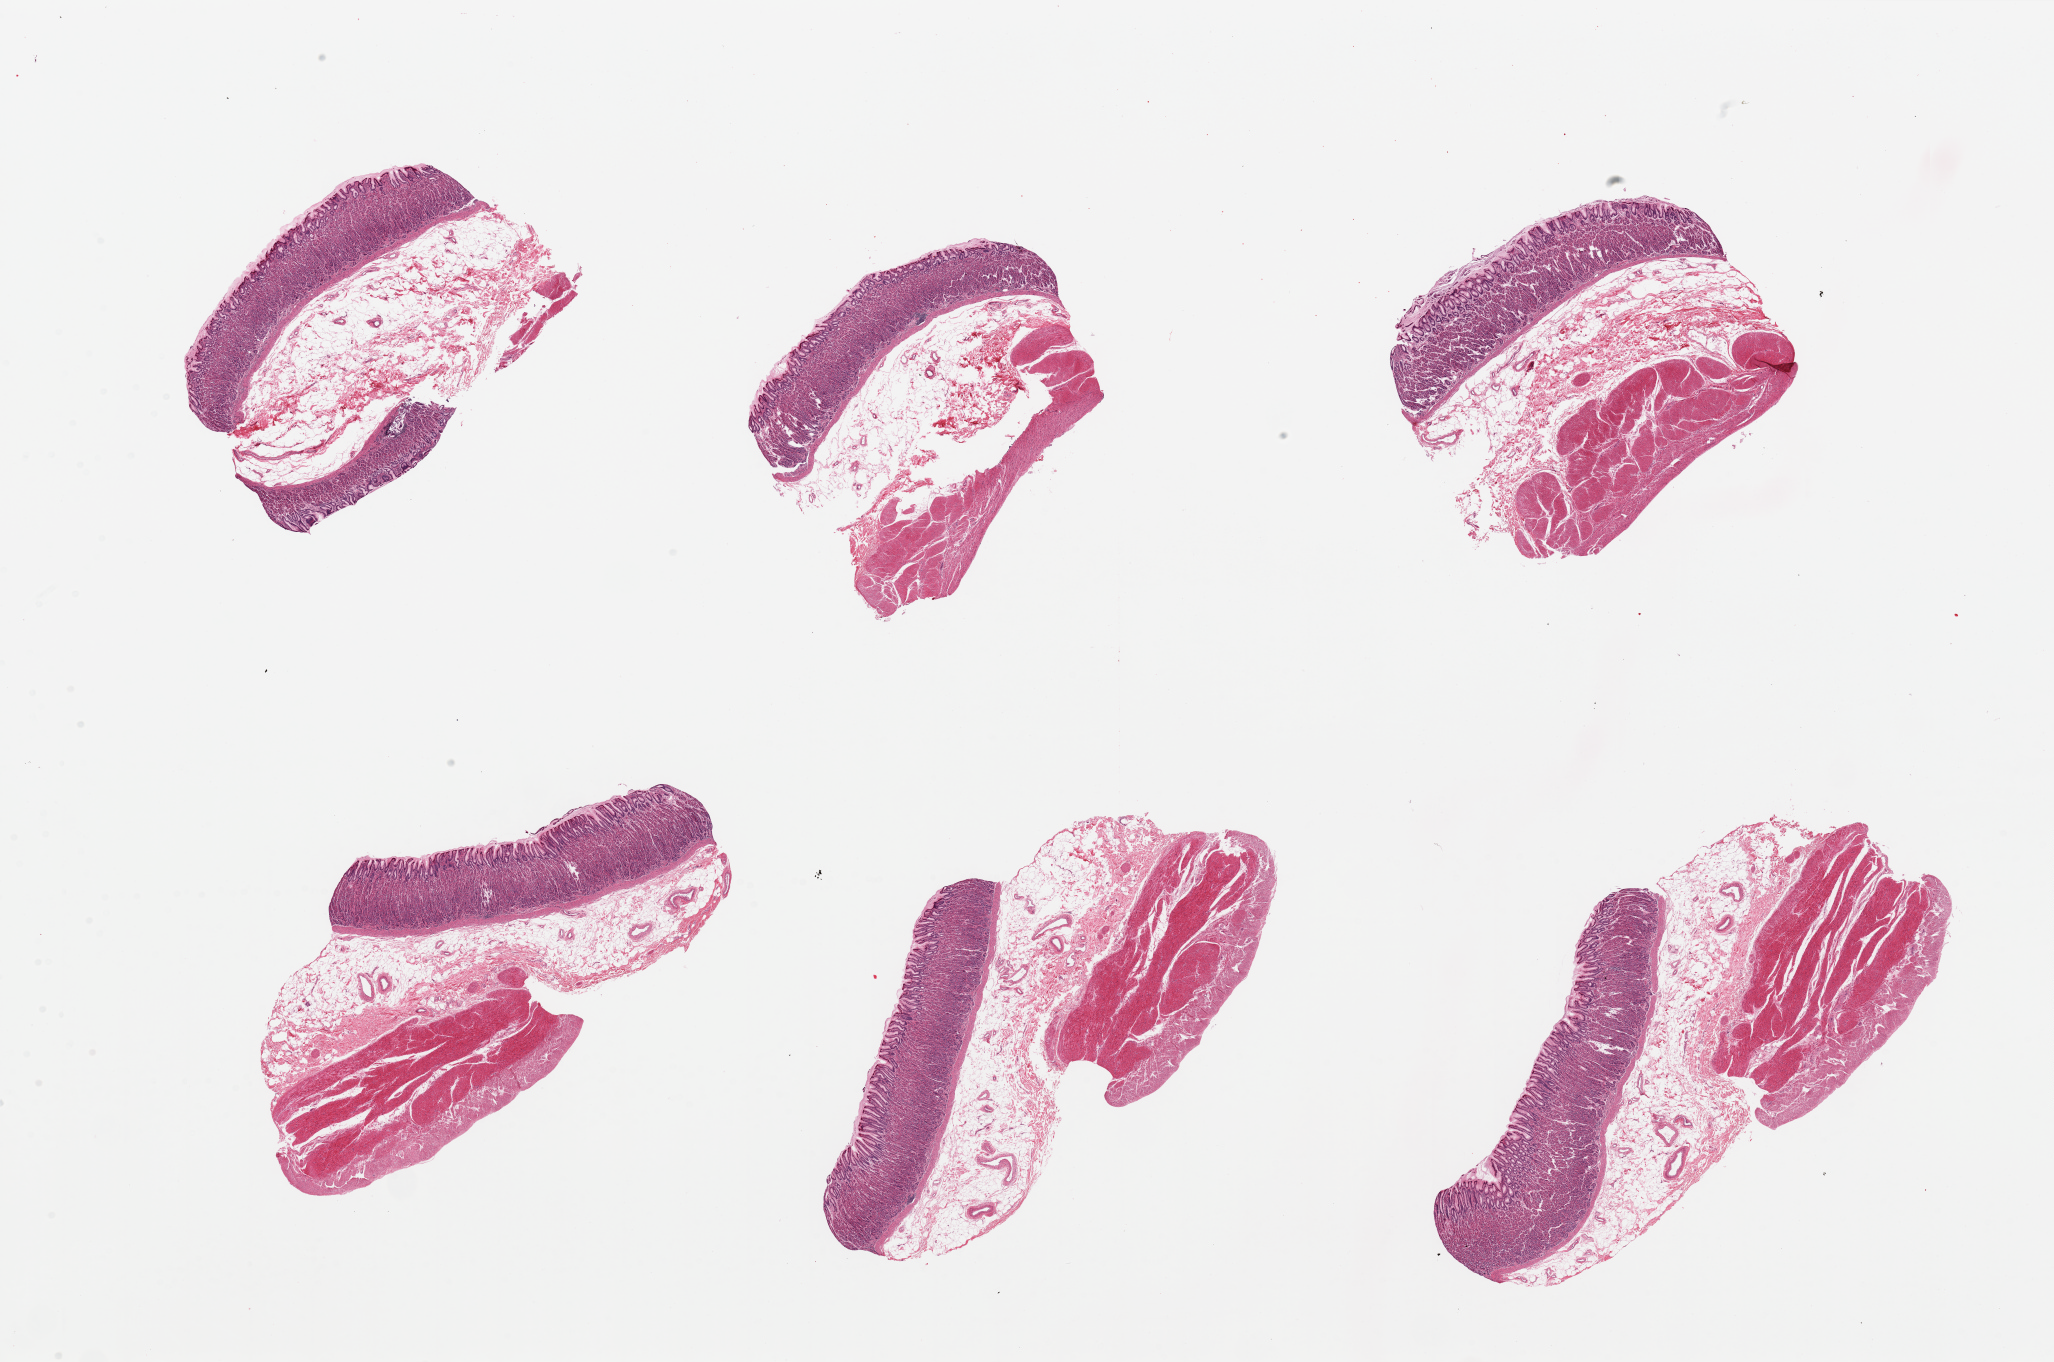
Digitized hematoxylin and eosin (H&E)-stained section, shown as a low-resolution overview of the whole scanned area (about 32.5 x 21.5 mm); PAXgene-fixed paraffin-embedded (PFPE) section; sampled site (target tissue): stomach; tissue donor sample.
Review note (as recorded): 6 pieces.